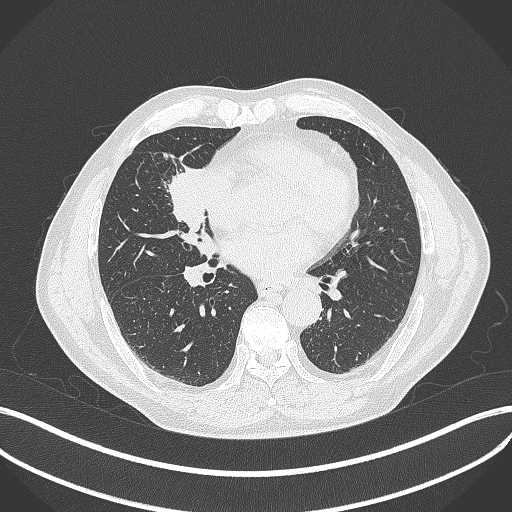
Chest CT, one axial slice. Position 184 of 429 along the scan axis. Reconstruction kernel B70f. 120 kVp. Lung window (W 1500 / L -600 HU). 1 mm slice thickness. 512 × 512 image matrix, field of view 400 × 400 mm. Patient: male, 61 years. From the clinical record (not read from this slice): clinical TNM (as recorded): T2b N1 M0.
Outlined on this slice (rectangle marked by the reading radiologist):
- lung tumour (recorded histology: squamous cell carcinoma): bounding box (x1, y1, x2, y2) in pixels: (157, 157, 212, 244)